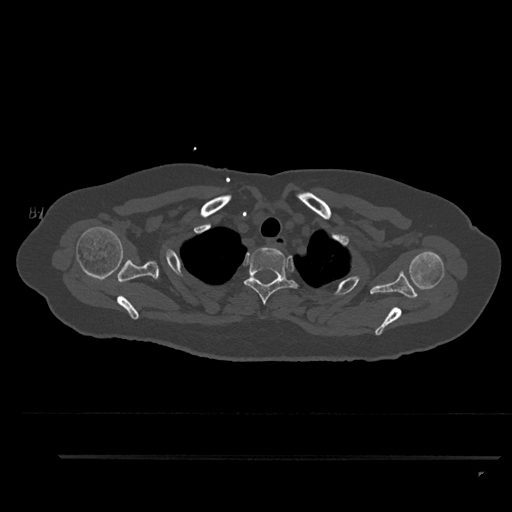
CT including the spine, one axial slice. Slice 724 of 797 in the series (ordered by position). Bone window (W 1800 / L 400 HU). 512 × 512 image matrix, field of view 408 × 408 mm. Female patient, age 44 years. Case-level facts recorded for this patient, not image findings: primary cancer: renal.
Outlined on this slice (semi-automatic segmentation, software-assisted and operator-edited):
- T2 vertebra: box from (x=244, y=247) to (x=298, y=305) px